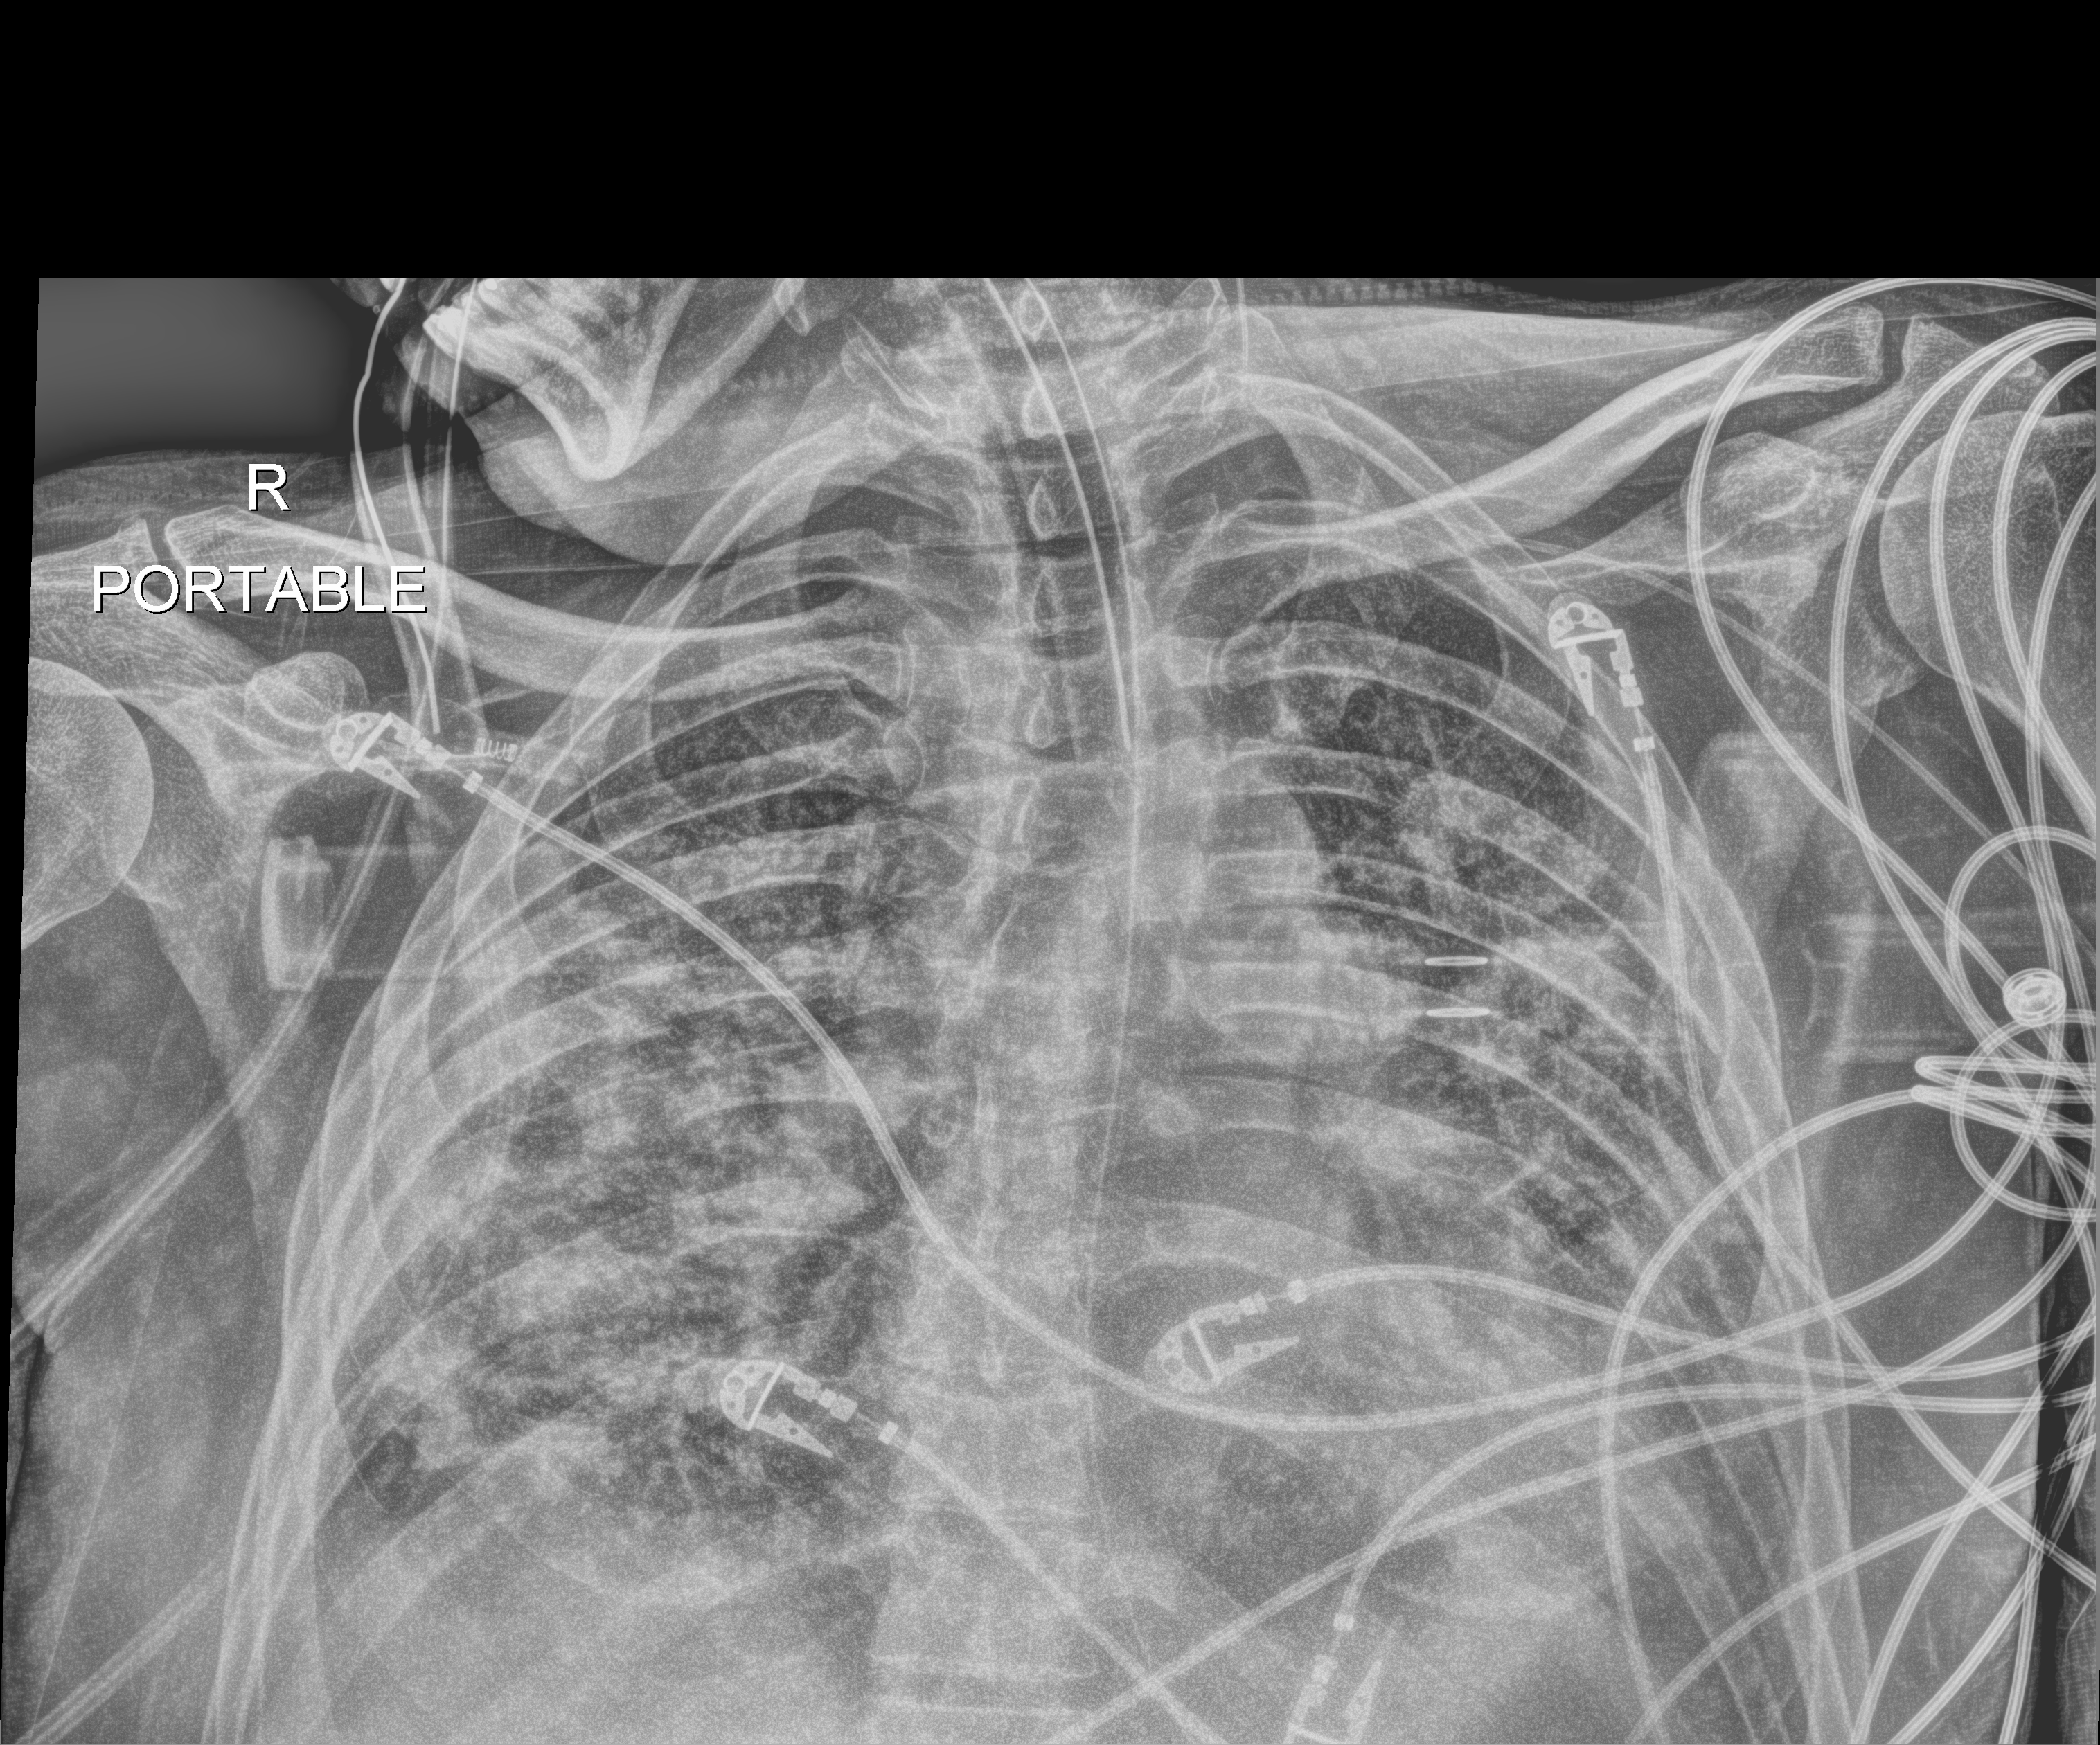
Portable chest radiograph, anteroposterior (AP) projection. Male patient hospitalised with COVID-19, age 18–59 years.
Hospital-stay facts (about this admission, not read from this image; timing relative to this image not recorded): other chronic lung disease (admission record): no; admitted to intensive care during this hospital stay: yes; mechanically ventilated during this hospital stay: yes.